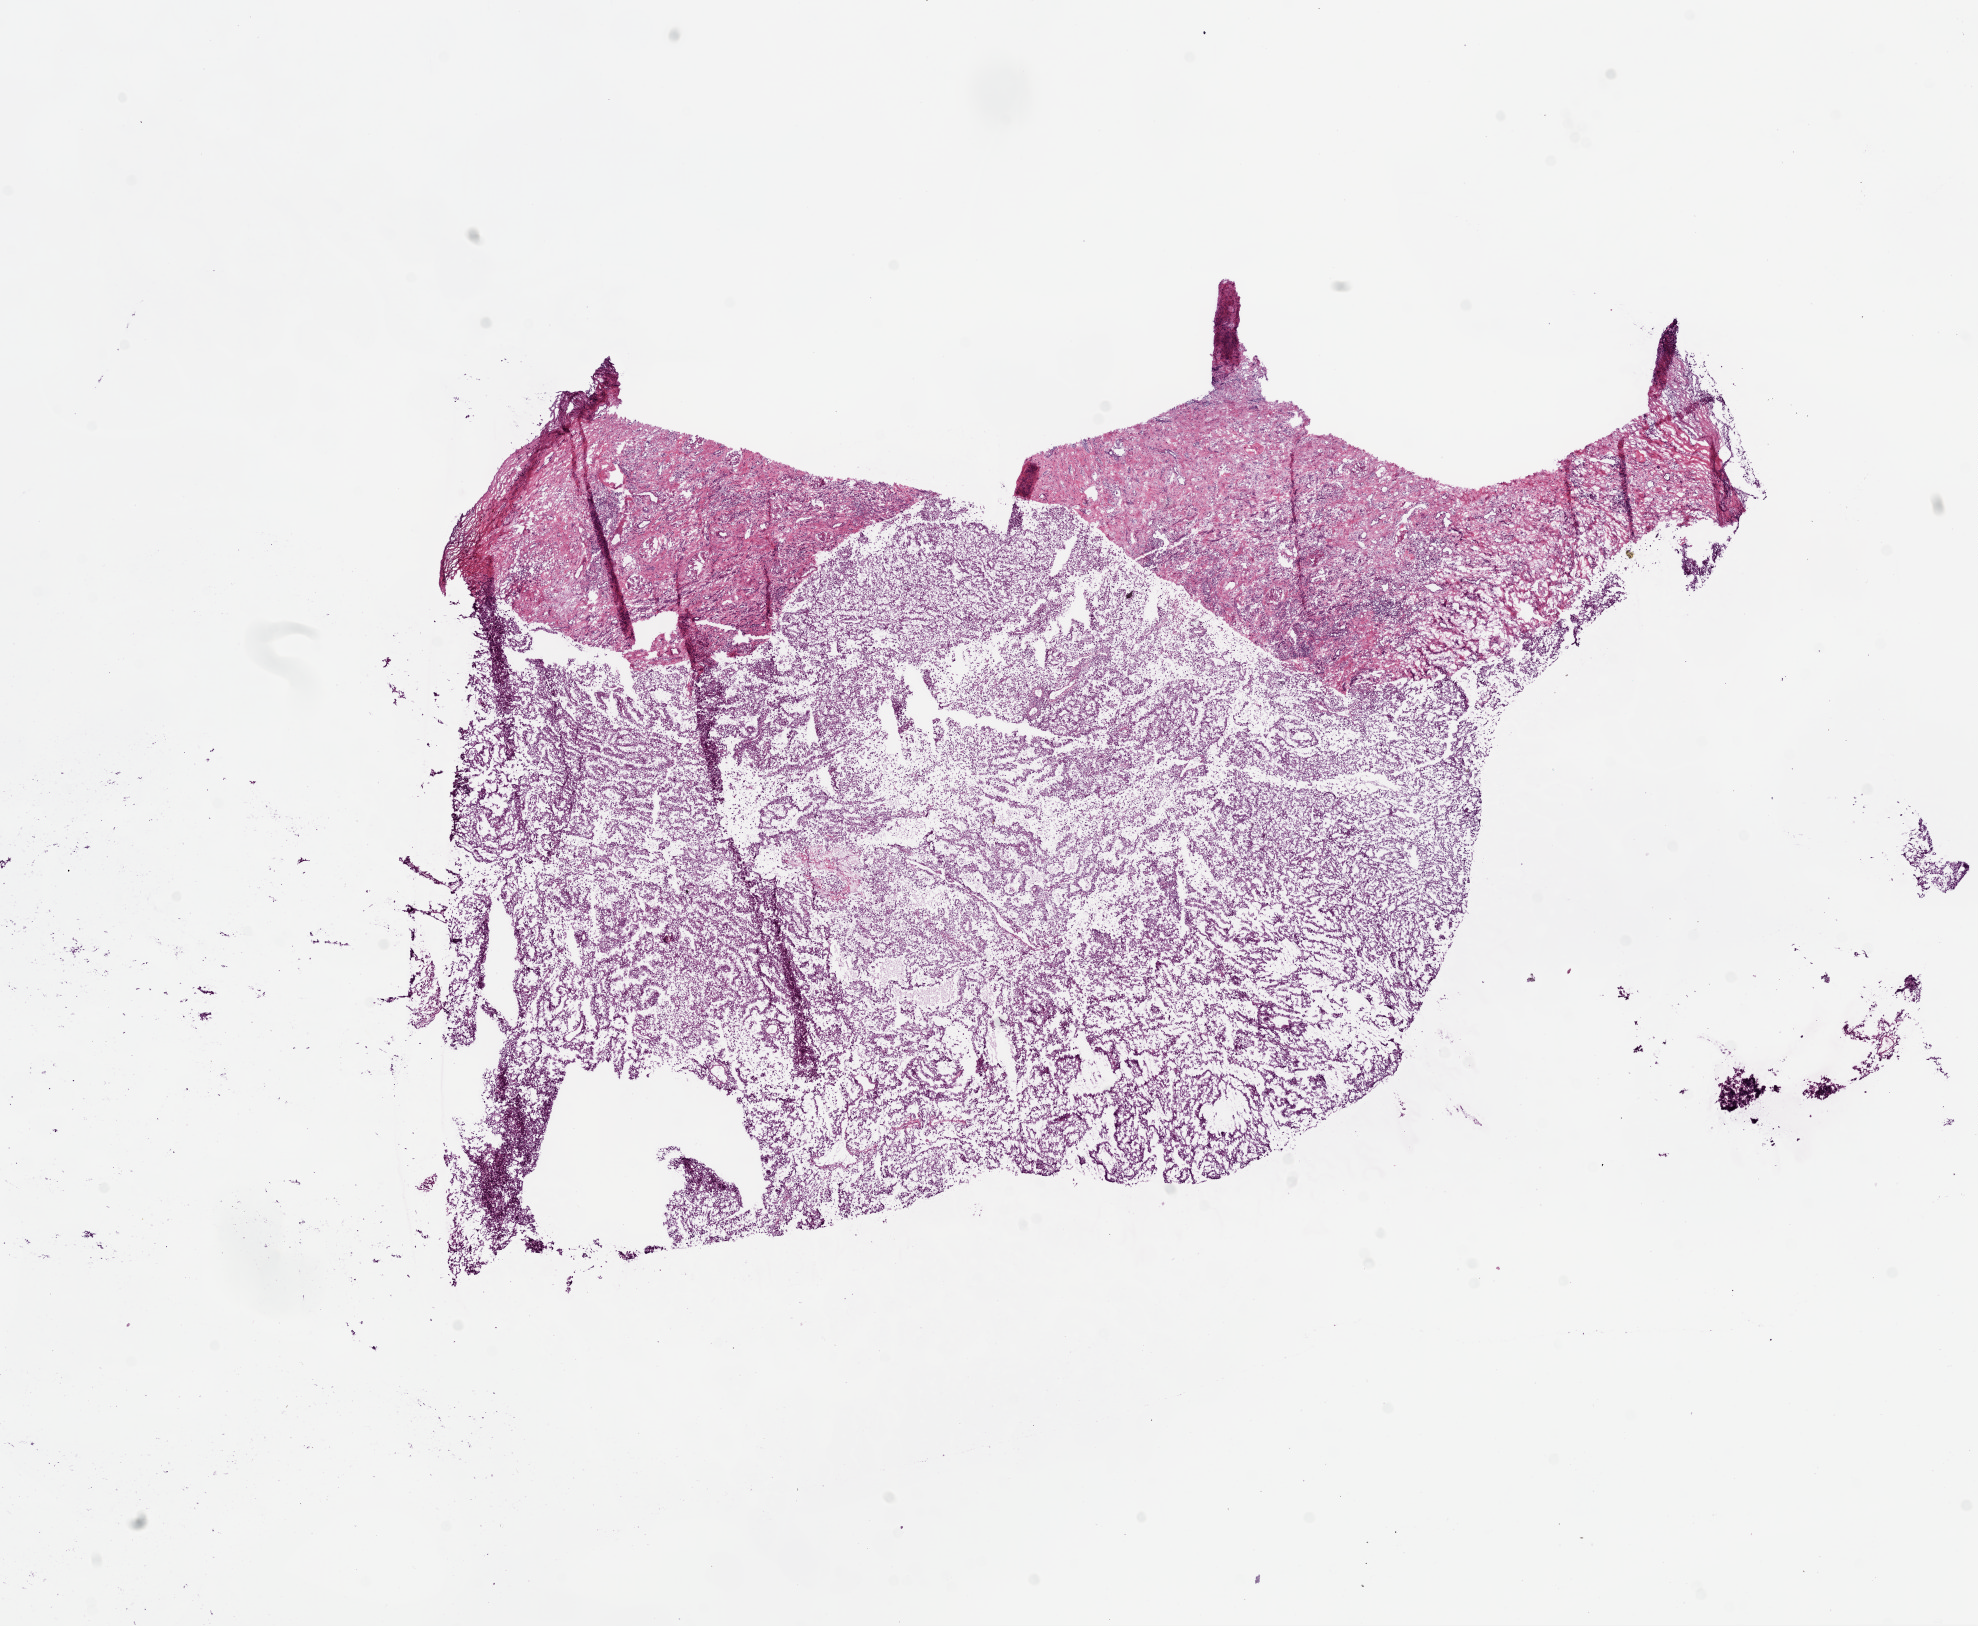
Whole-slide histology image, H&E-stained — whole scanned area (about 16.0 x 13.1 mm, slide scanned at 20x) shown as a low-resolution overview; frozen section from the bottom of the tissue portion; kidney, primary tumour sample. Female patient; age at initial diagnosis 64 years. Histologic grade: G2 (moderately differentiated). Slide review estimates, as recorded: tumour cells 80%, tumour nuclei 80%, normal cells 0%, stromal cells 20%, necrosis 0%. Infiltration values recorded for this section: lymphocyte infiltration 5%, monocyte infiltration 0%, neutrophil infiltration 0%.
Diagnosis: Clear cell adenocarcinoma, NOS. Lymph nodes positive (case pathology): 0 of 7 examined. Laterality: left. AJCC pathologic stage: I (7th edition).